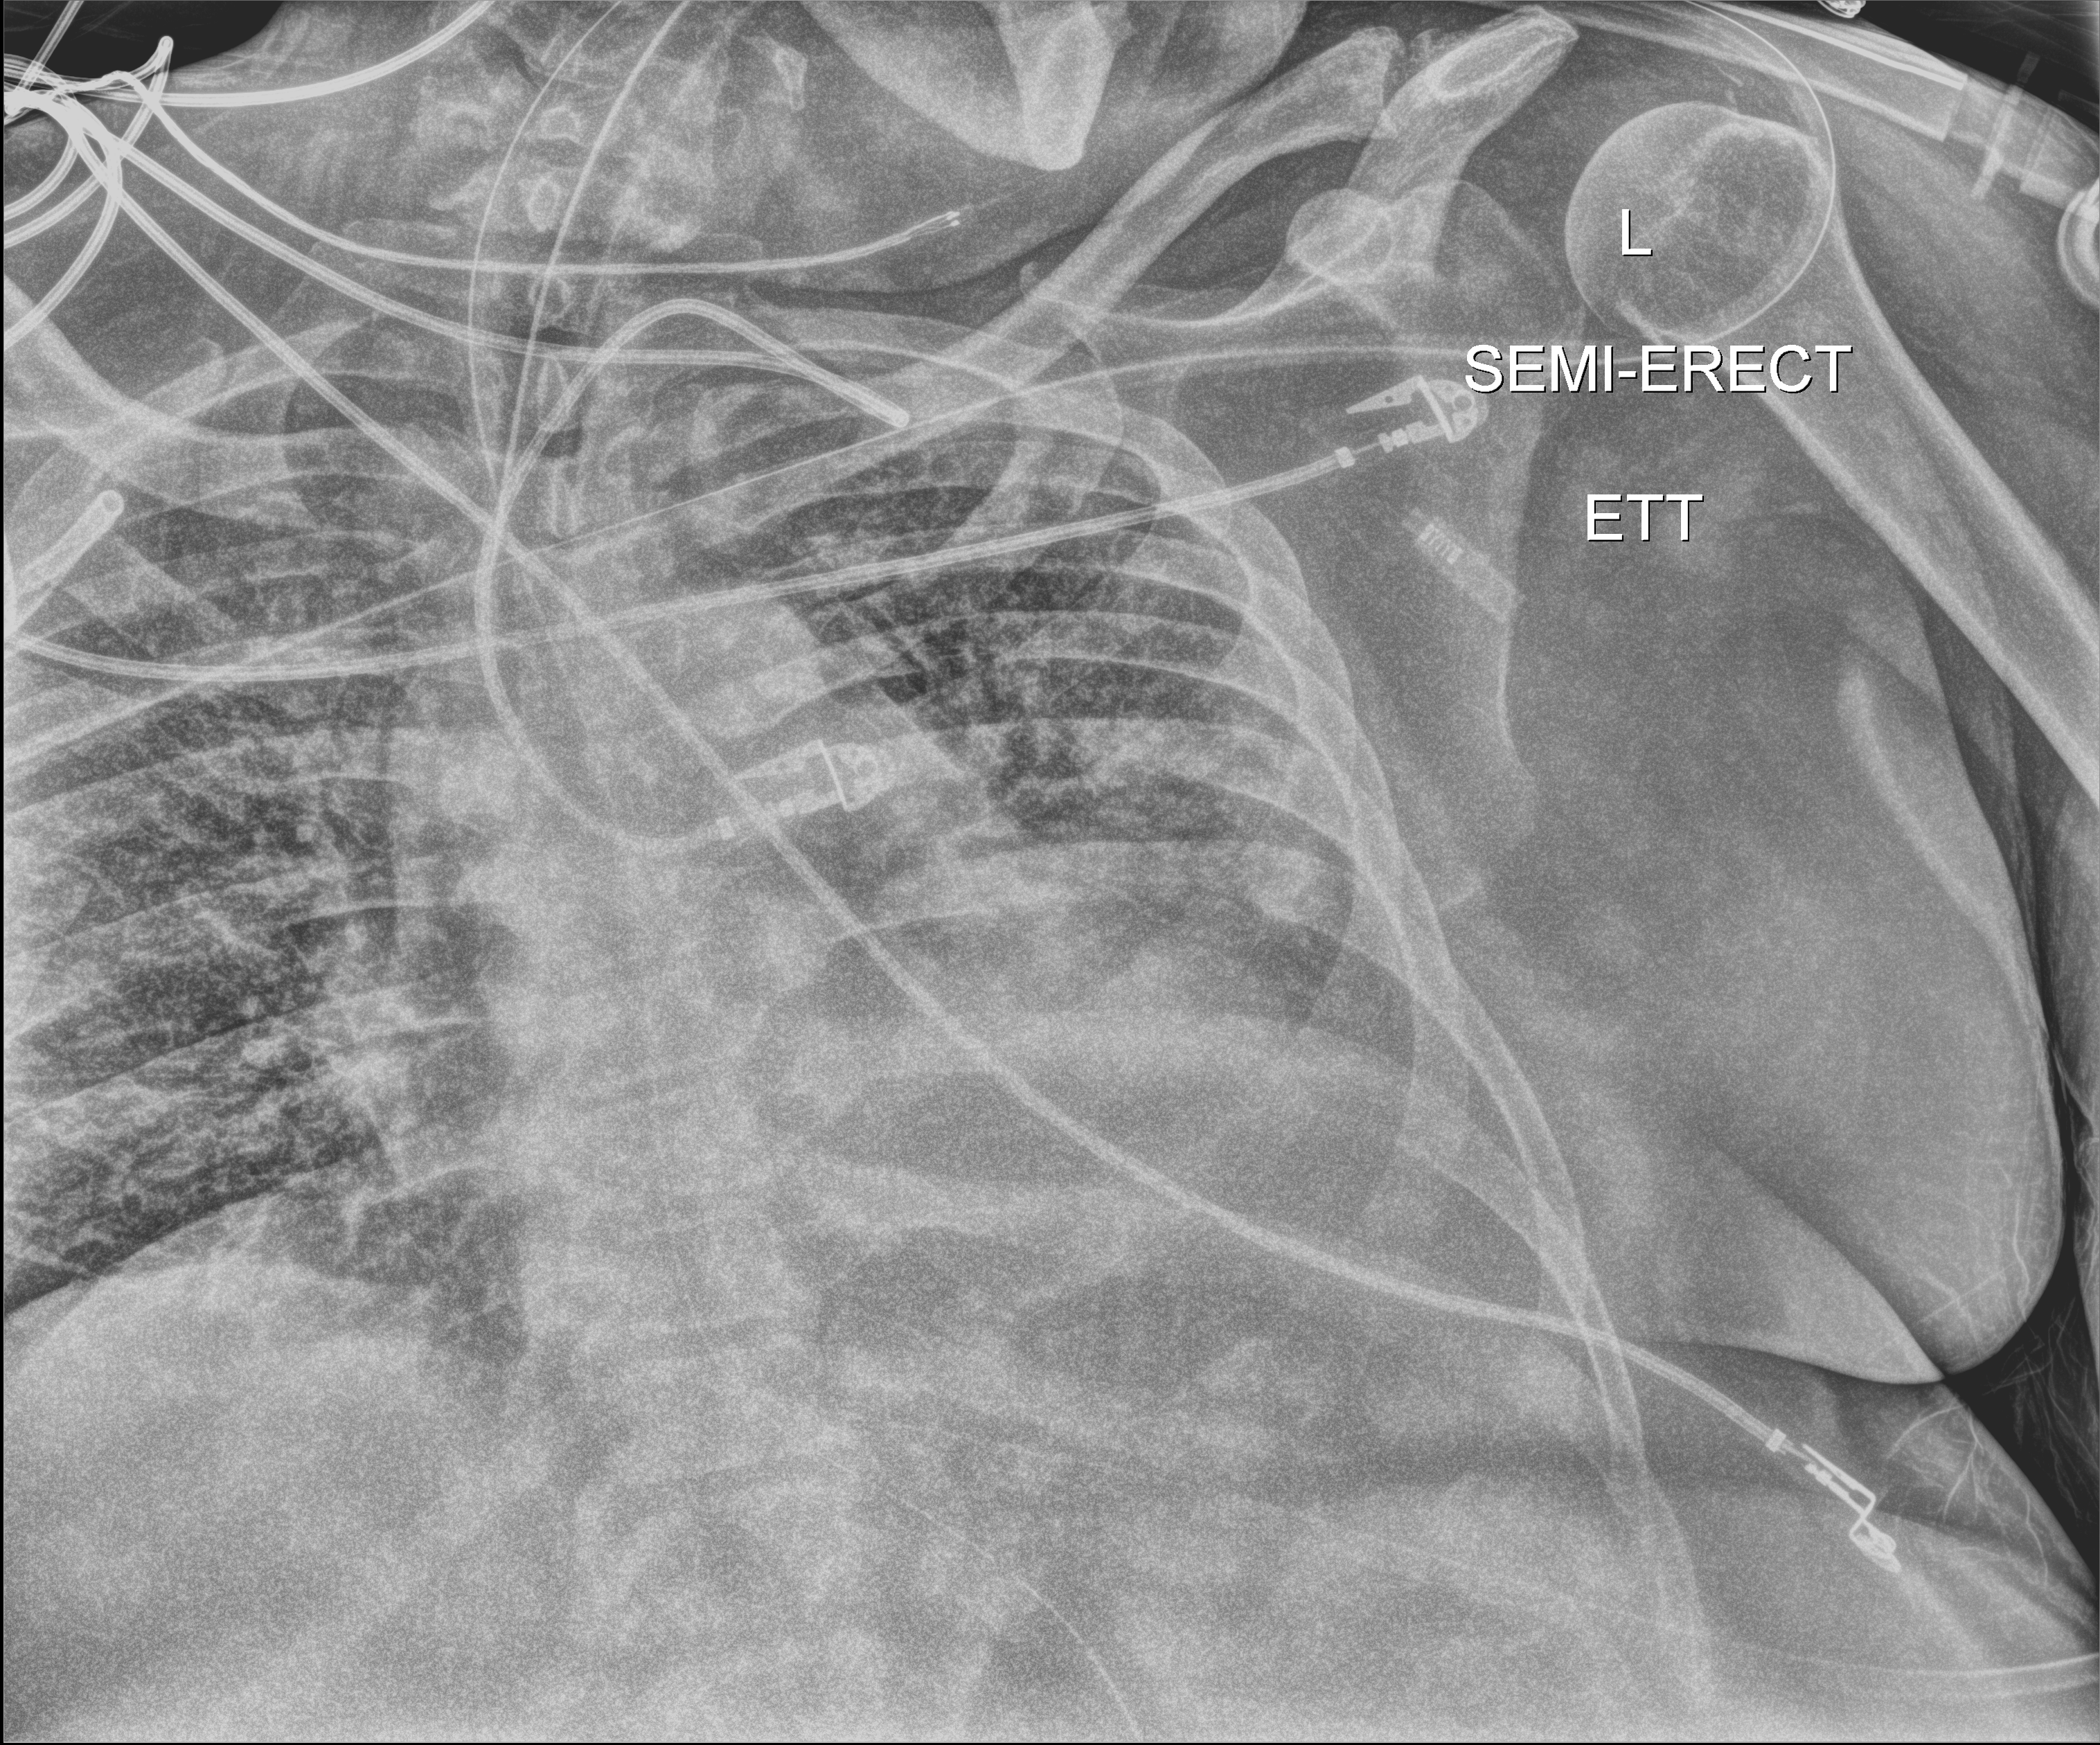
Chest radiograph, anteroposterior (AP) projection. Patient hospitalised with COVID-19; male, aged 60–74 years.
Hospital-stay facts (about this admission, not read from this image; timing relative to this image not recorded):
- other chronic lung disease (admission record): no
- mechanically ventilated during this hospital stay: yes